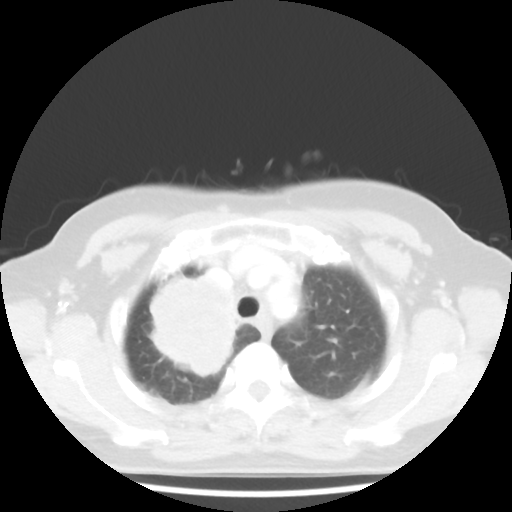
Chest CT, one axial slice. Slice 36 of 44 in the series (ordered by position). Reconstruction kernel STANDARD. 100 kVp. Lung window (W 1500 / L -600 HU). 512 × 512 image matrix, field of view 316 × 316 mm. Patient: female, 62 years. From the clinical record (not read from this slice): clinical TNM (as recorded): T3 N0 M0.
Structures marked on this image (rectangle marked by the reading radiologist):
- lung tumour (recorded histology: small cell carcinoma): bounding box [x1, y1, x2, y2] px = [131, 262, 248, 386]